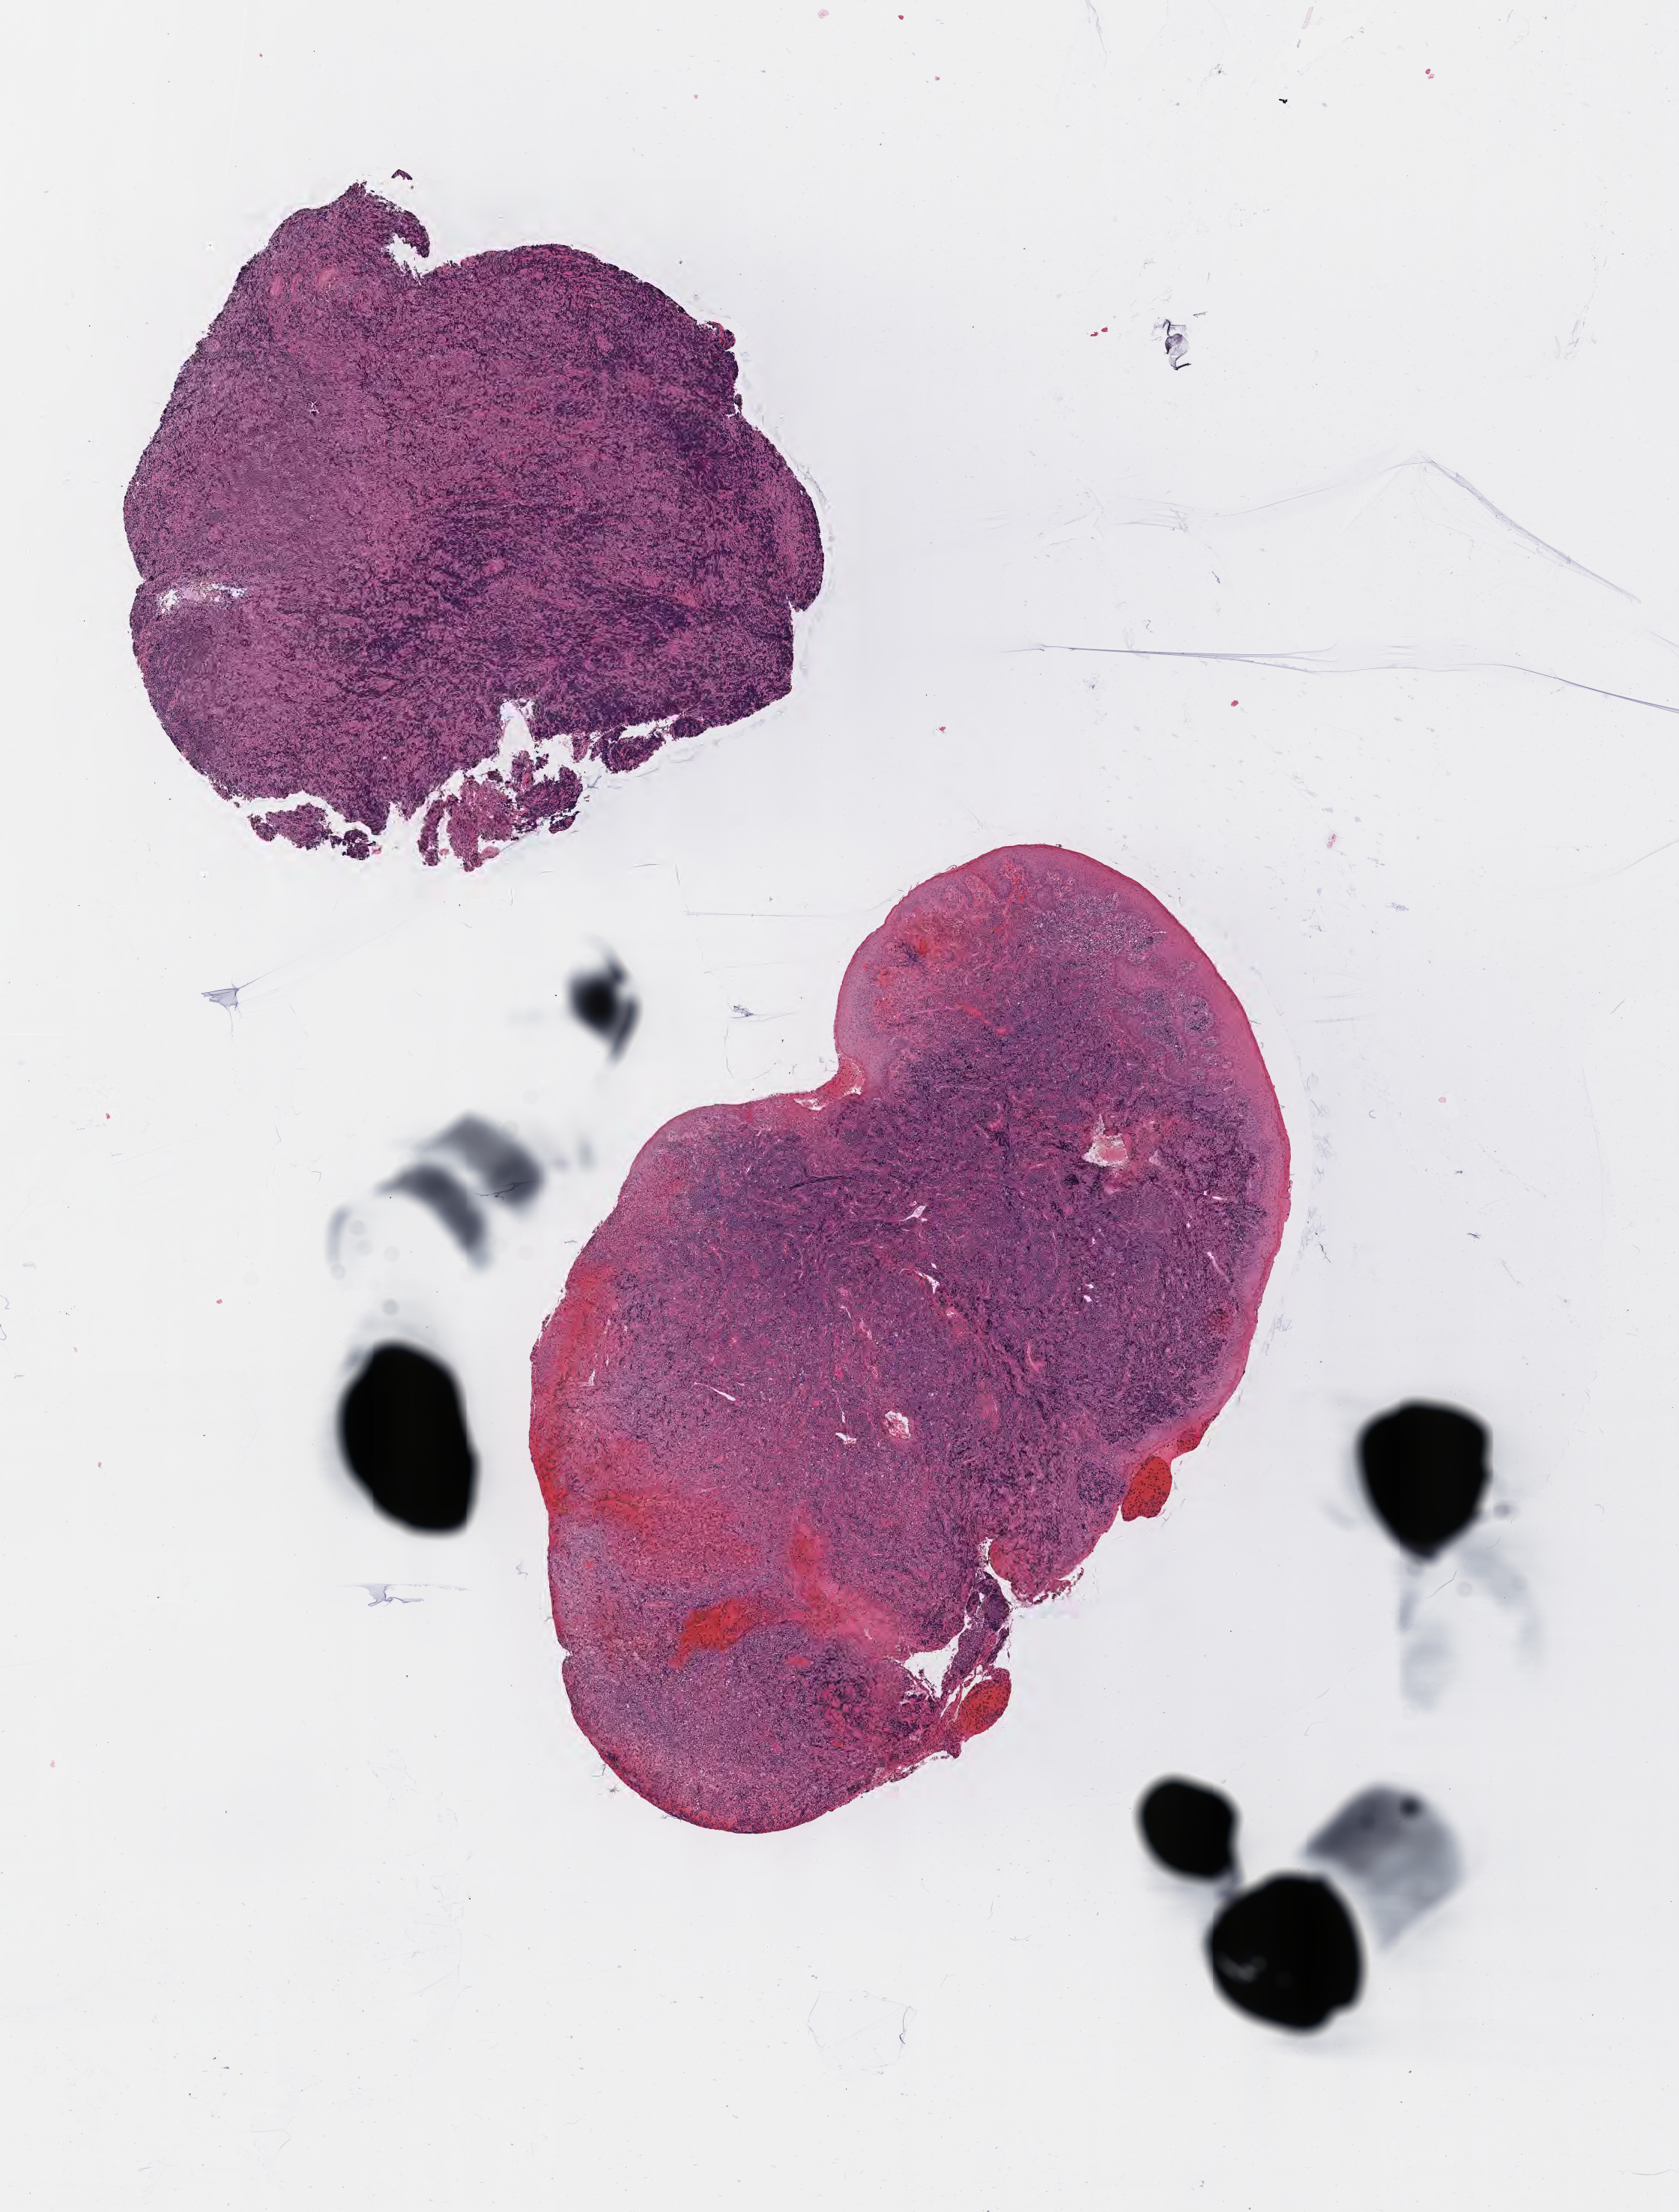
Haematoxylin and eosin whole-slide image, low-resolution overview of the scanned area, about 9.1 x 11.9 mm. Specimen: tumor tissue. Anatomic site: mandible. Patient: female, age at initial diagnosis 8 years.
- histologic diagnosis: Burkitt lymphoma, NOS